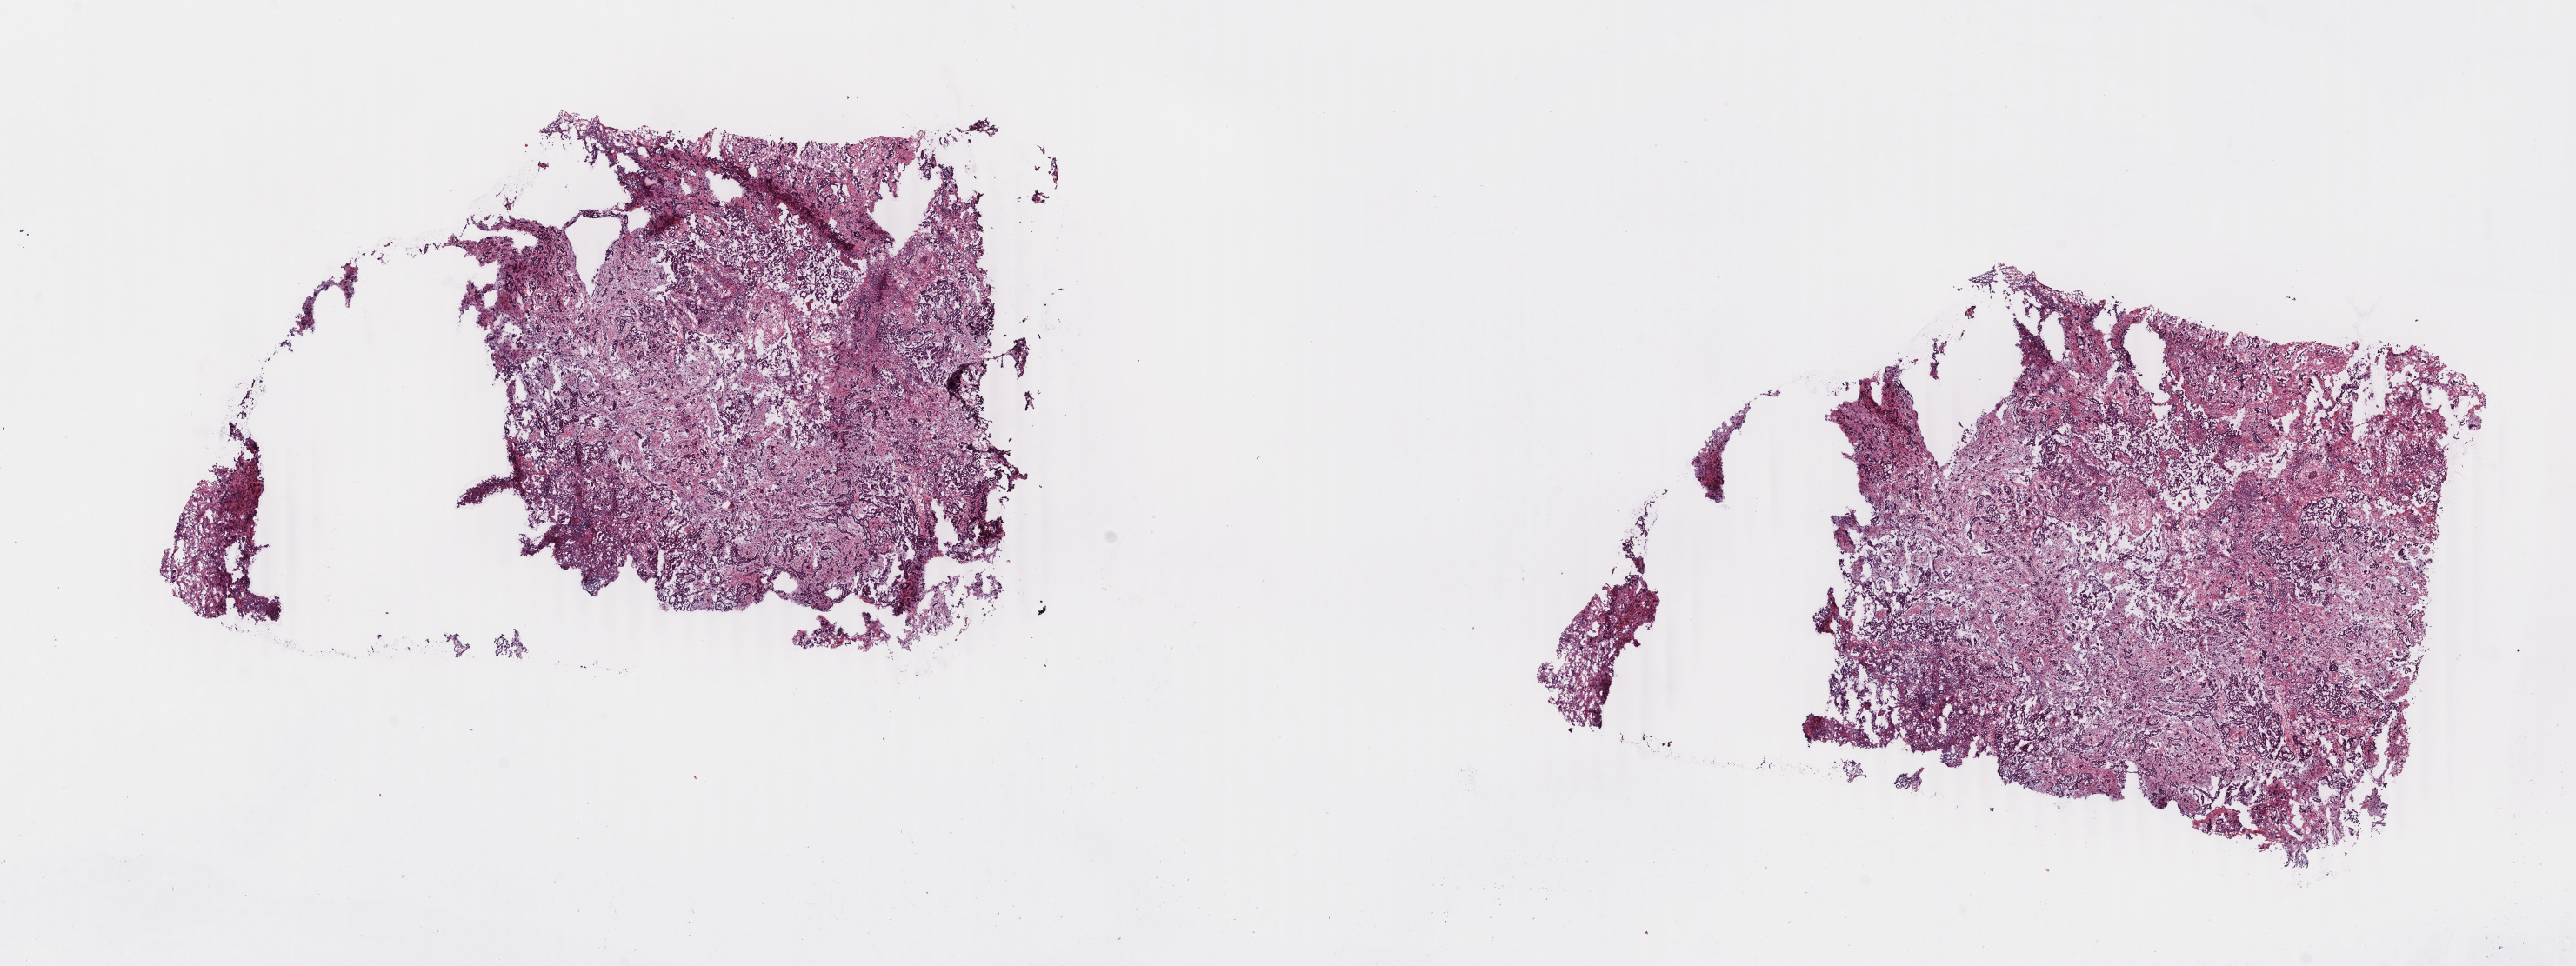
Hematoxylin and eosin (H&E) stained whole-slide image, shown as a low-resolution overview of the whole scanned area (about 23.6 x 8.8 mm, slide scanned at 40x). Frozen section from the top of the tissue portion. Mesothelium, primary tumour sample. Male, age 53 years at initial diagnosis. Pathologist review of this section (percent, as recorded): tumour cells 100%, tumour nuclei 75%, normal cells 0%, stromal cells 0%, necrosis 0%. Infiltration values recorded for this section: lymphocyte infiltration 2%, monocyte infiltration 0%, neutrophil infiltration 0%.
* diagnosis: Epithelioid mesothelioma, malignant (pleura, NOS)
* laterality: left
* AJCC pathologic stage: III